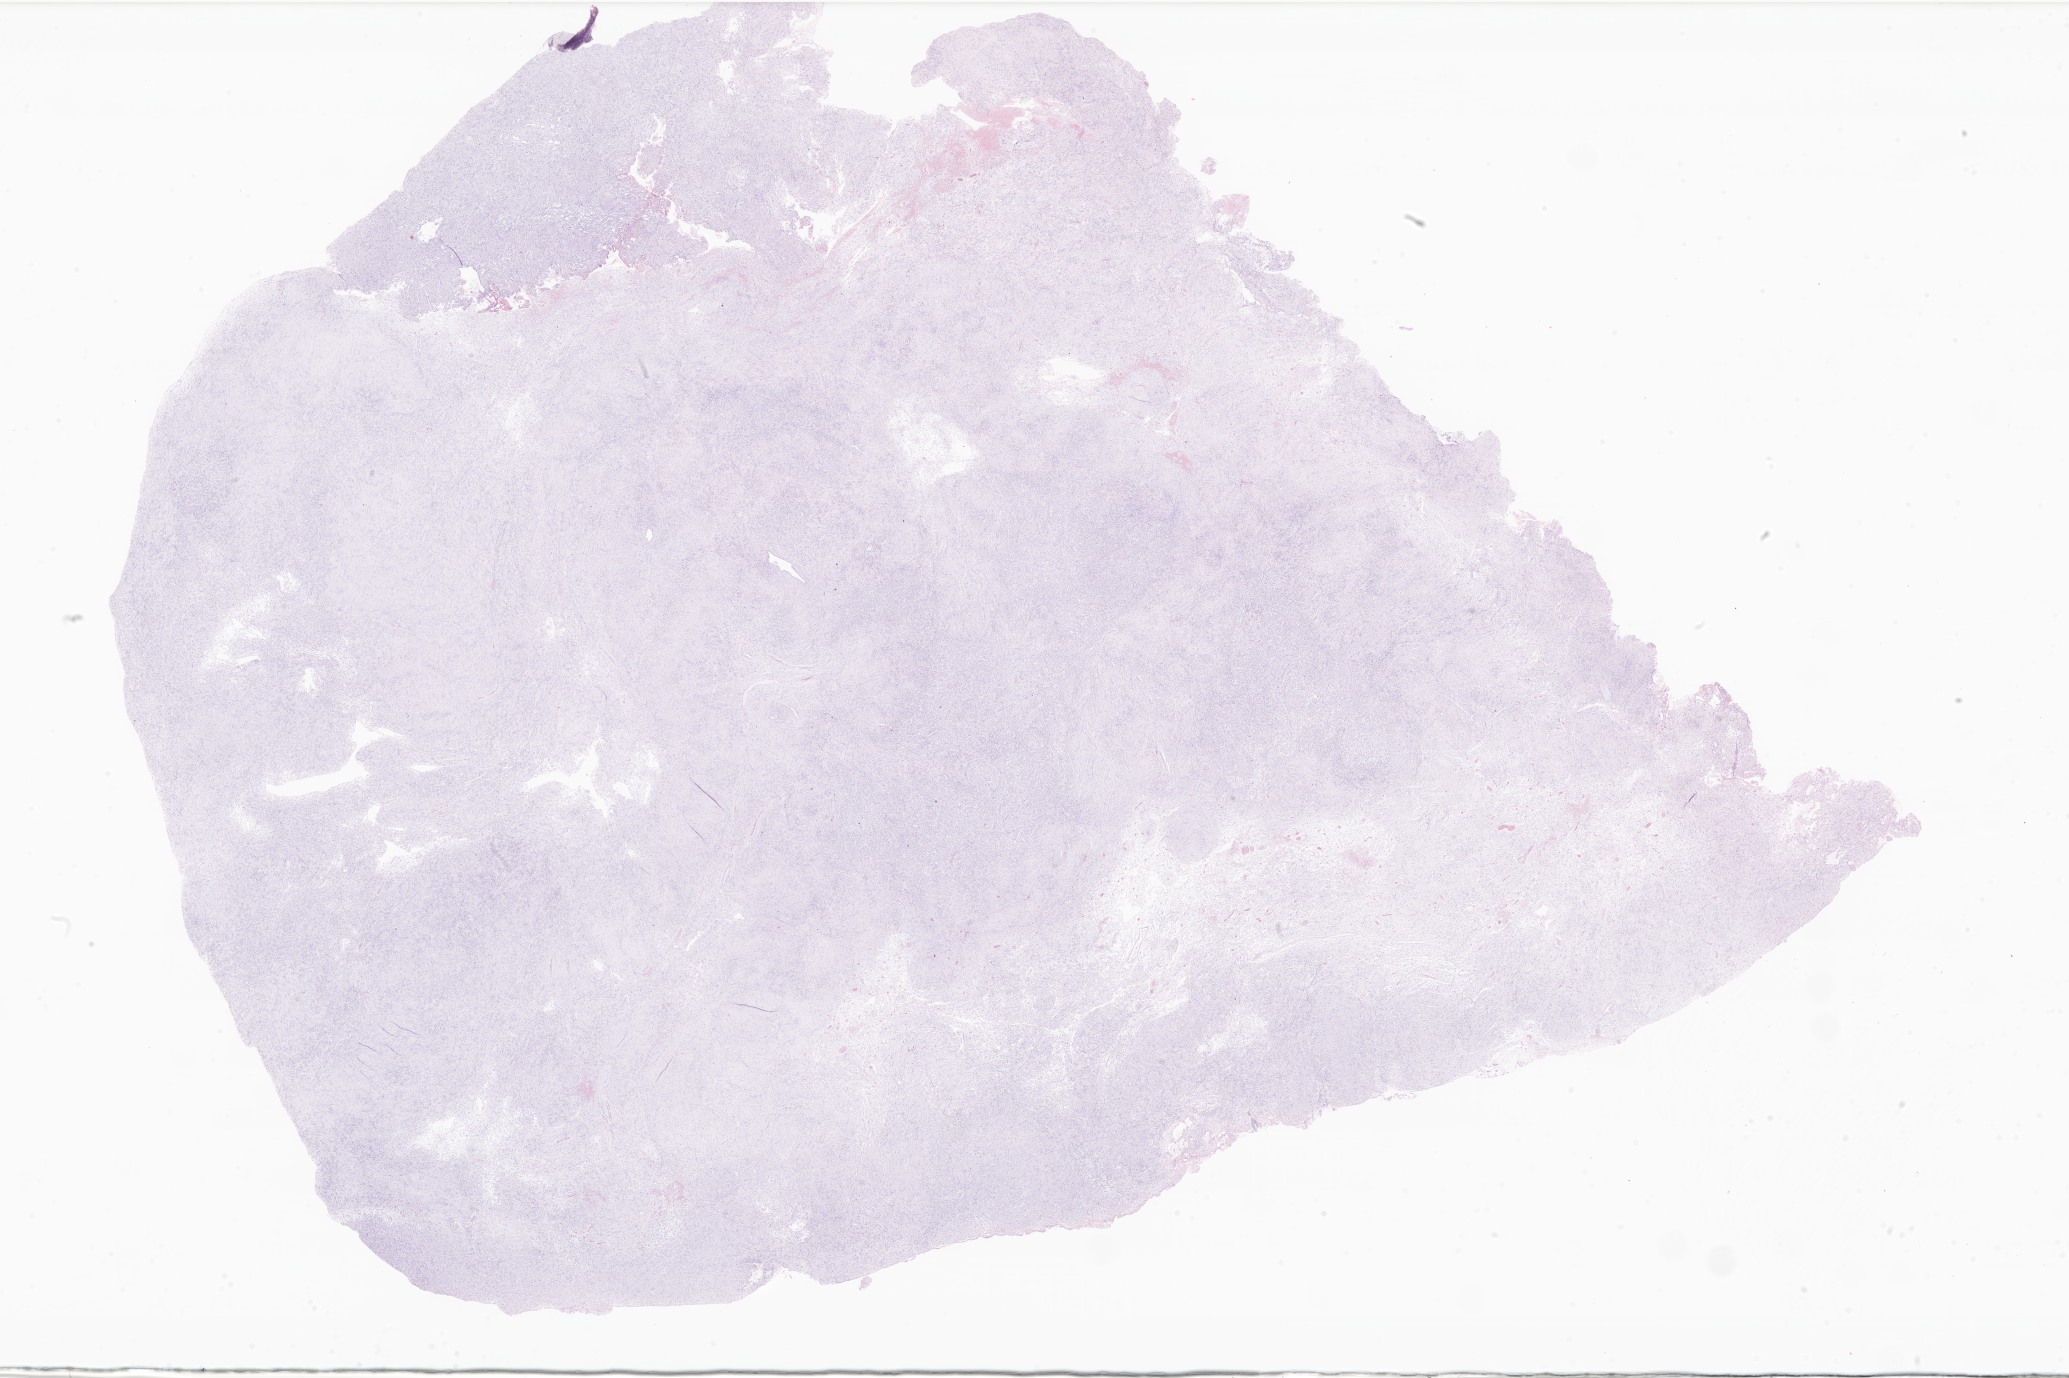
Hematoxylin and eosin (H&E) whole-slide image of tumor tissue from the brain, low-resolution overview of the scanned area, about 34.9 x 23.2 mm. FFPE section. Male patient, age 37 months (3 years 1 month).
Recorded diagnosis: Neoplasm, uncertain whether benign or malignant.